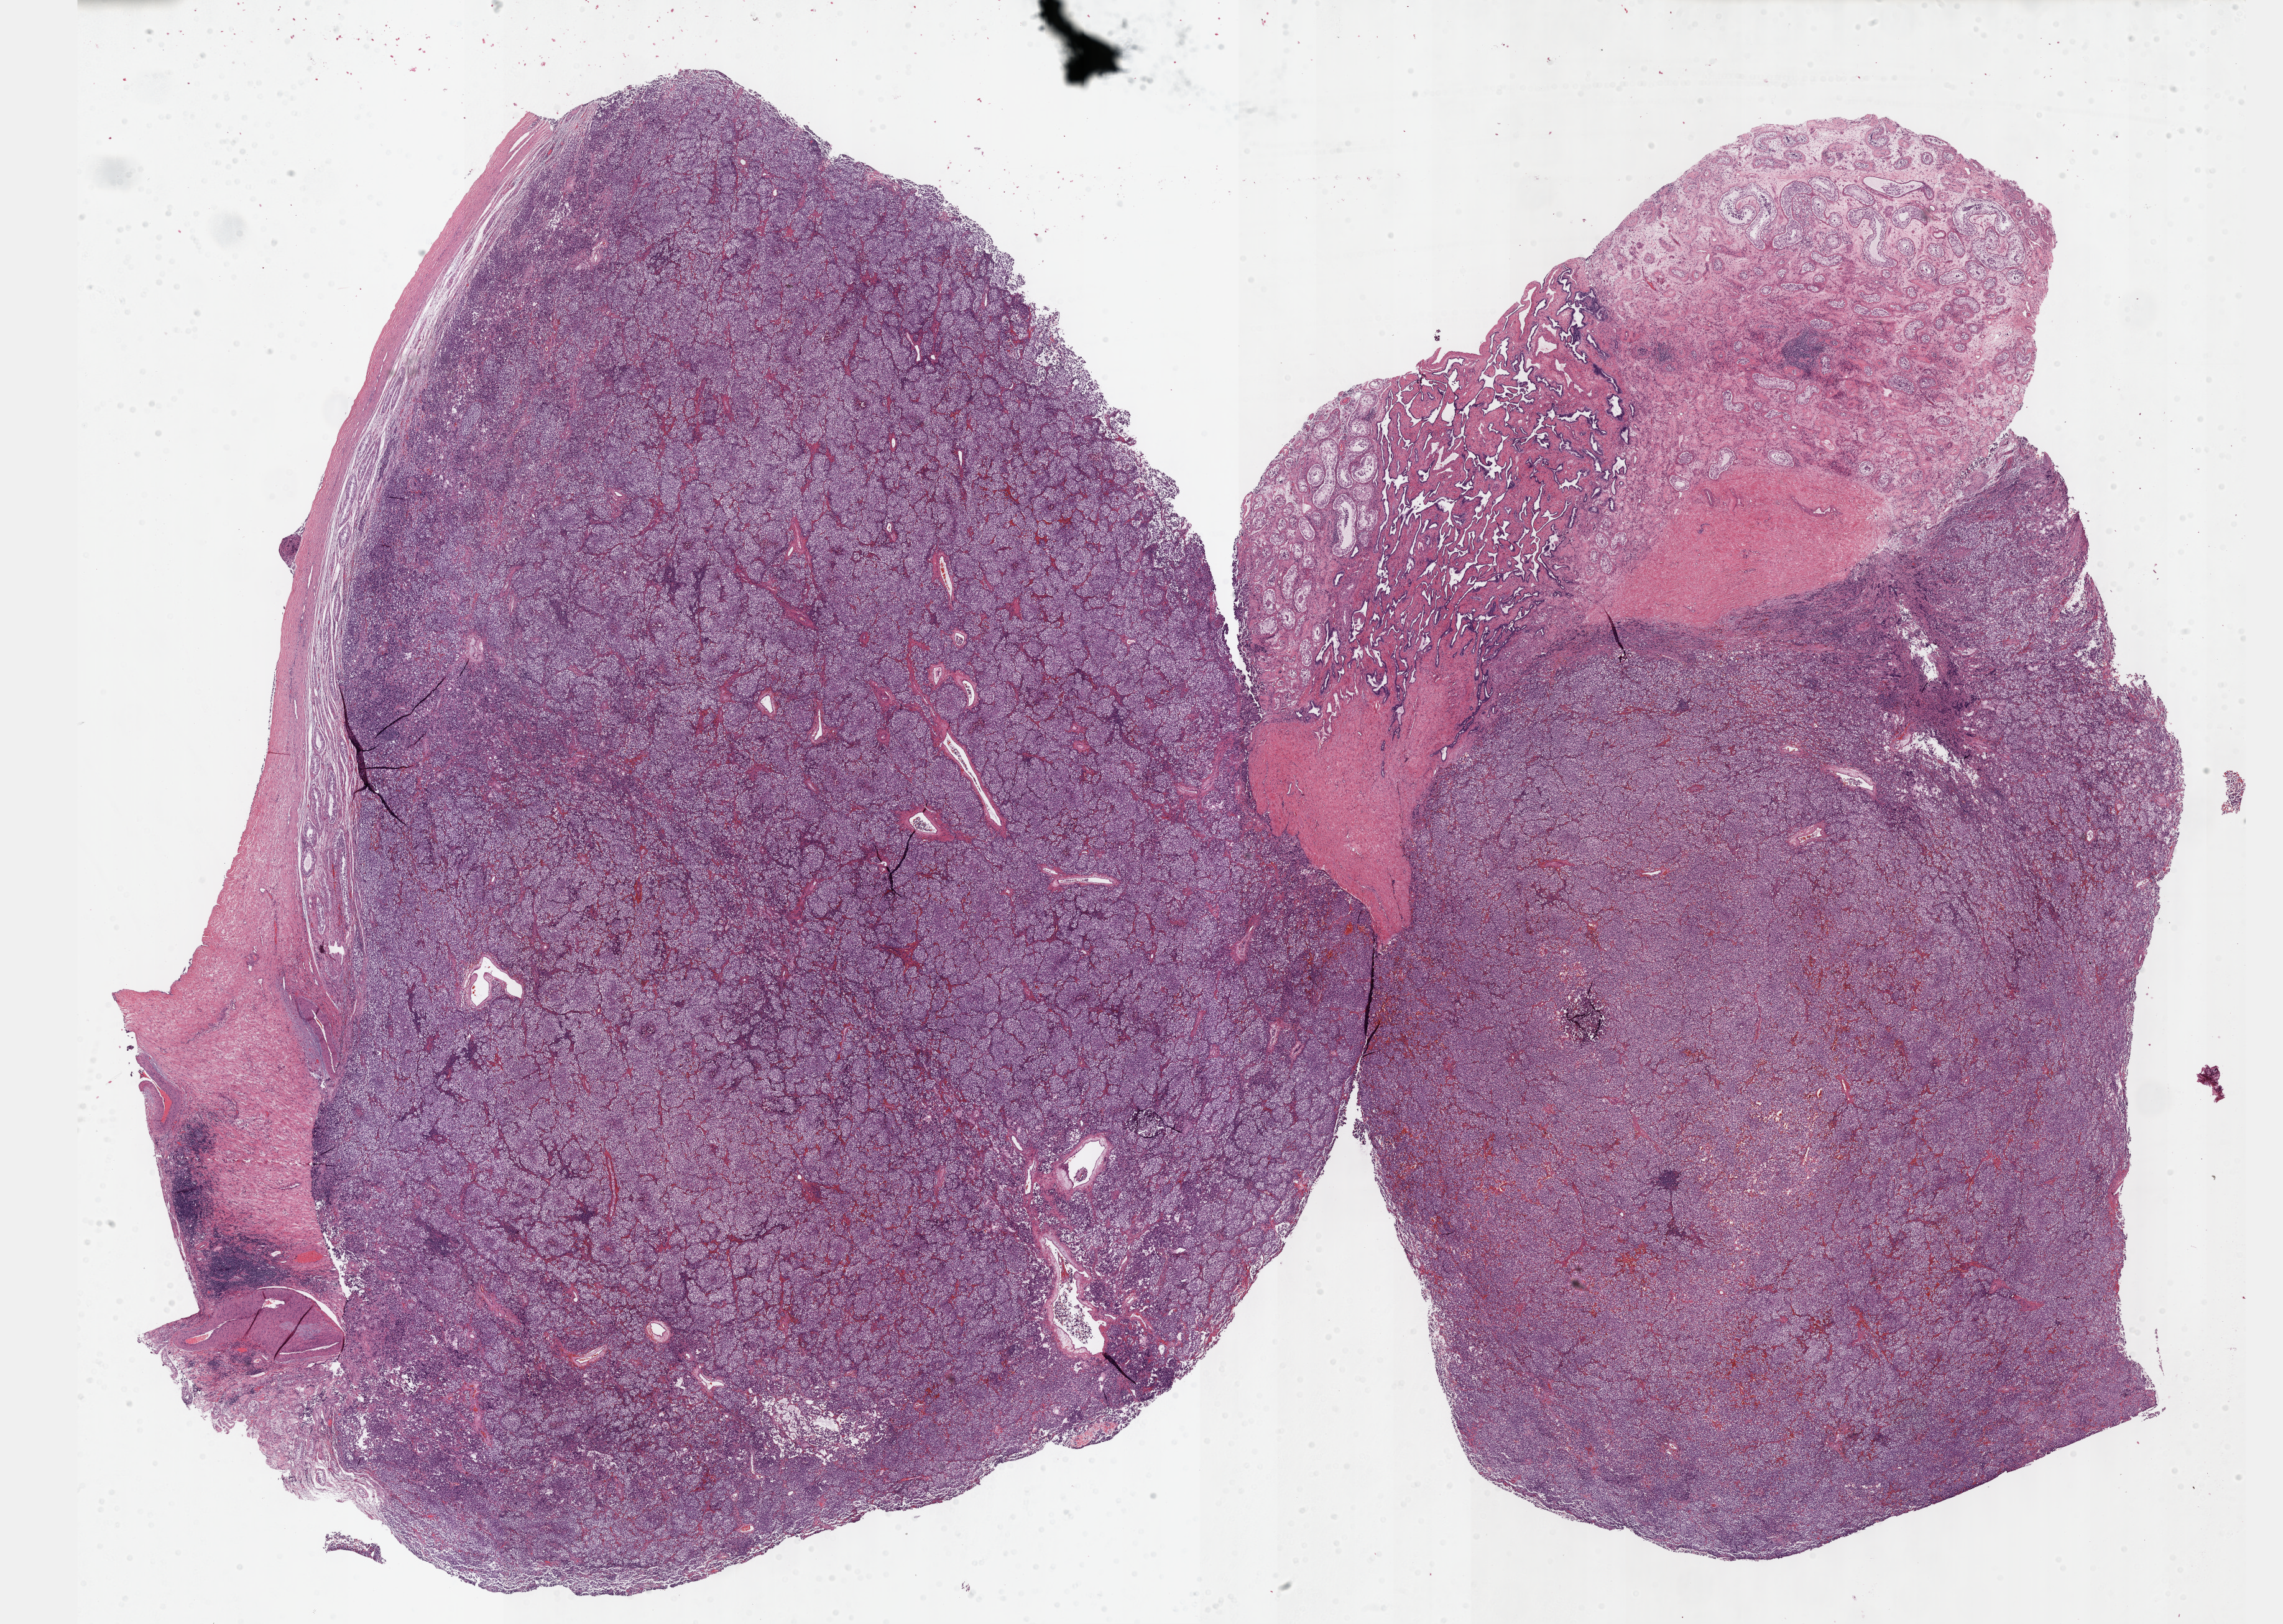
Hematoxylin and eosin (H&E) stained whole-slide image, low-resolution overview of the scanned area, about 29.7 x 21.1 mm. FFPE section. Primary tumour sample from the testis. Male patient; age at initial diagnosis 37 years.
Diagnosis: Seminoma, NOS. AJCC pathologic stage: IS (7th edition).